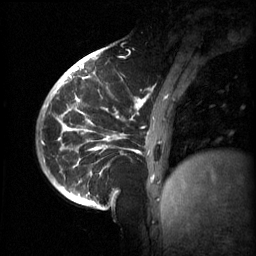
Breast MRI (dynamic contrast-enhanced), one sagittal slice; slice 16 of 60 in the series (ordered by position); 3 images stored at this slice position (order not interpretable as contrast timing); 1.5 T; TE 4.2 ms, TR 11 ms; 2 mm slice thickness; 256 × 256 image matrix, field of view 220 × 220 mm. Female patient, age 51 years.
Structures marked on this image (semi-automatic segmentation, software-assisted and operator-edited):
- analysis volume of interest (the breast-tissue region the enhancement analysis was run in; not a lesion): bounding box [x1, y1, x2, y2] px = [63, 80, 187, 201]
- tumour enhancement mask (voxels above the 70 % enhancement threshold inside the analysis volume of interest): [69, 80, 153, 183]